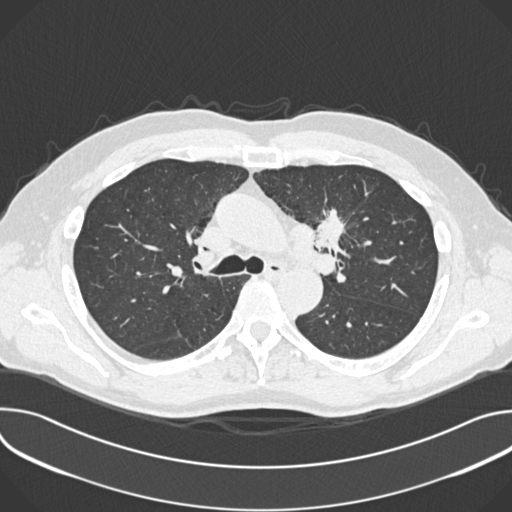
Low-dose screening chest CT, one axial slice. Slice 252 of 361 in the series (ordered by position). Reconstruction kernel B30f. Lung window (W 1500 / L -600 HU). 1 mm slice thickness. 512 × 512 image matrix.
Outlined on this slice (manually delineated by an expert):
- lesion 1 (tumor, upper lobe of left lung): bounding box <316,209,345,248> (left, top, right, bottom; pixels)